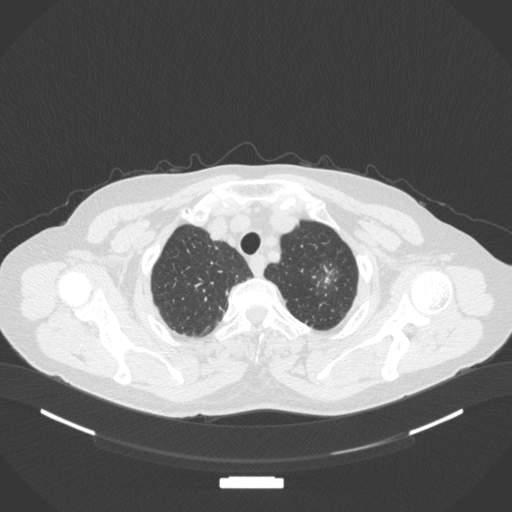
Chest CT, one axial slice; slice 316 of 369 in the series (ordered by position); lung window (W 1500 / L -600 HU); 1 mm slice thickness; 512 × 512 image matrix. Female patient, age 64 years. Case-level facts recorded for this patient, not image findings: clinical TNM (as recorded): T1c N0 M0.
Structures marked on this image (bounding box drawn by a radiologist):
- lung tumour (recorded histology: adenocarcinoma): bounding box (x1, y1, x2, y2) in pixels: (307, 257, 351, 302)